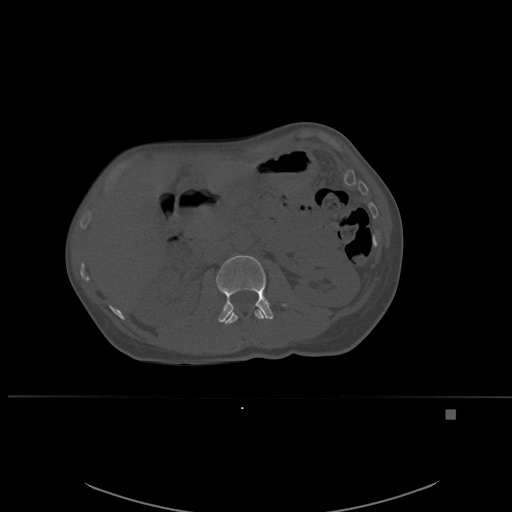
CT including the spine, one axial slice. Position 244 of 537 along the scan axis. Bone window (W 1800 / L 400 HU). 512 × 512 image matrix. Patient: female, 45 years. From the clinical record (not read from this slice): primary cancer: lung.
Outlined on this slice (semi-automatic segmentation, software-assisted and operator-edited):
- L1 vertebra: box from (x=223, y=308) to (x=265, y=324) px
- L2 vertebra: (x=216, y=255)–(x=286, y=322)